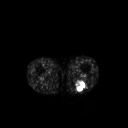
FDG PET of an extremity soft-tissue mass (from a PET/CT study), one axial slice. Slice 199 of 267 in the series (ordered by position). 3.27 mm slice thickness. 128 × 128 image matrix, field of view 500 × 500 mm. Patient: male, 54 years. Case-level facts recorded for this patient, not image findings: histological type: synovial sarcoma; site of the primary tumour: left poplietal fossa.
Annotated regions visible in this slice (expert contour drawn on MRI and transferred to this co-registered scan by the dataset authors):
- gross tumour volume (mass): bounding box (x1, y1, x2, y2) in pixels: (75, 80, 86, 91)